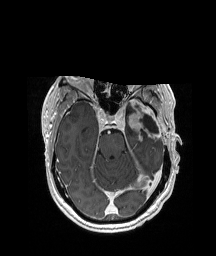
Brain MRI from a brain-tumour surgery series, one axial slice. Slice 132 of 208 in the series (ordered by position). T1-weighted post-contrast. 216 × 256 image matrix, field of view 228 × 270 mm. Case-level facts recorded for this patient, not image findings: histopathology: Glioblastoma; WHO grade: 4.
Outlined on this slice (outlined manually by an expert reader):
- previous resection cavity: bounding box (x1, y1, x2, y2) in pixels: (134, 105, 158, 134)
- tumour: (133, 99, 158, 144)